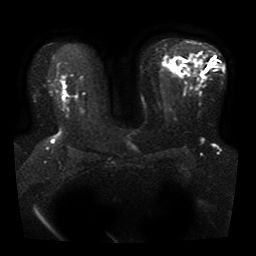
Breast MRI, one axial slice. Position 21 of 41 along the scan axis. Diffusion-weighted series; image 2 of 4 stored at this slice position (different b-values; order by instance number). 1.5 T. 5 mm slice thickness. 256 × 256 image matrix, field of view 330 × 330 mm. Female patient.
Annotated regions visible in this slice (outlined manually by an expert reader):
- tumour on diffusion-weighted imaging: bounding box [x1, y1, x2, y2] px = [63, 91, 66, 101]